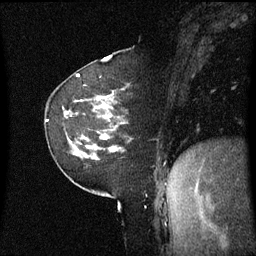
Breast MRI (dynamic contrast-enhanced), one sagittal slice. Position 18 of 60 along the scan axis. Dynamic contrast-enhanced series, image 2 of 3 at this slice position (ordered by acquisition). 1.5 T. TE 4.2 ms, TR 8.4 ms. 256 × 256 image matrix, field of view 220 × 220 mm. Patient: female, 60 years. From the clinical record (not read from this slice): setting: breast cancer imaged before/during neoadjuvant chemotherapy; receptor status: triple-negative.
Annotated regions visible in this slice (semi-automatically segmented with operator editing):
- analysis volume of interest (the breast-tissue region the enhancement analysis was run in; not a lesion): bounding box <62,98,128,161> (left, top, right, bottom; pixels)
- tumour enhancement mask (voxels above the 70 % enhancement threshold inside the analysis volume of interest): <101,136,115,151>